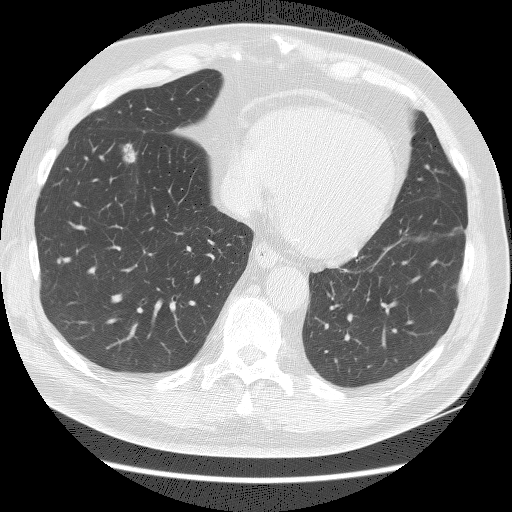
Low-dose screening chest CT, axial slice, baseline screening round, lung window (W 1500 / L -600 HU), 2.5 mm slice thickness, lung (sharp) reconstruction kernel (BONE), slice 112 of 161 in the series. Male participant, aged 65 years at enrolment. Current smoker at enrolment.
Lesion marked by an expert reader, bounding box [x1, y1, x2, y2] px = [105, 133, 151, 170]. The screening reader recorded 3 non-calcified nodules or masses ≥4 mm on this exam; which of them this box marks is not recorded. Participant outcome: lung cancer diagnosed 132 days after this screen — adenocarcinoma, NOS, right lower lobe, poorly differentiated (G3), stage IA (AJCC 6th edition), 10 mm at pathology.